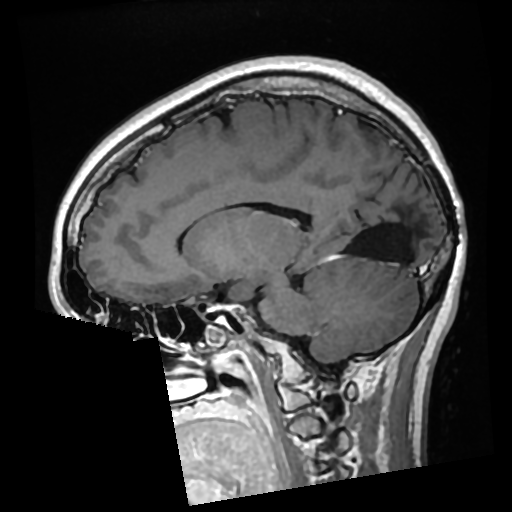
Brain MRI from a brain-tumour surgery series, one sagittal slice. Slice 120 of 276 in the series (ordered by position). T1-weighted post-contrast. 0.7 mm slice thickness. 512 × 512 image matrix, field of view 250 × 250 mm. Case-level facts recorded for this patient, not image findings: histopathology: Glioma with ependymal features; WHO grade: 2; tumour location: Left Parietal.
Outlined on this slice (outlined manually by an expert reader):
- previous resection cavity: bounding box [x1, y1, x2, y2] px = [349, 206, 412, 260]